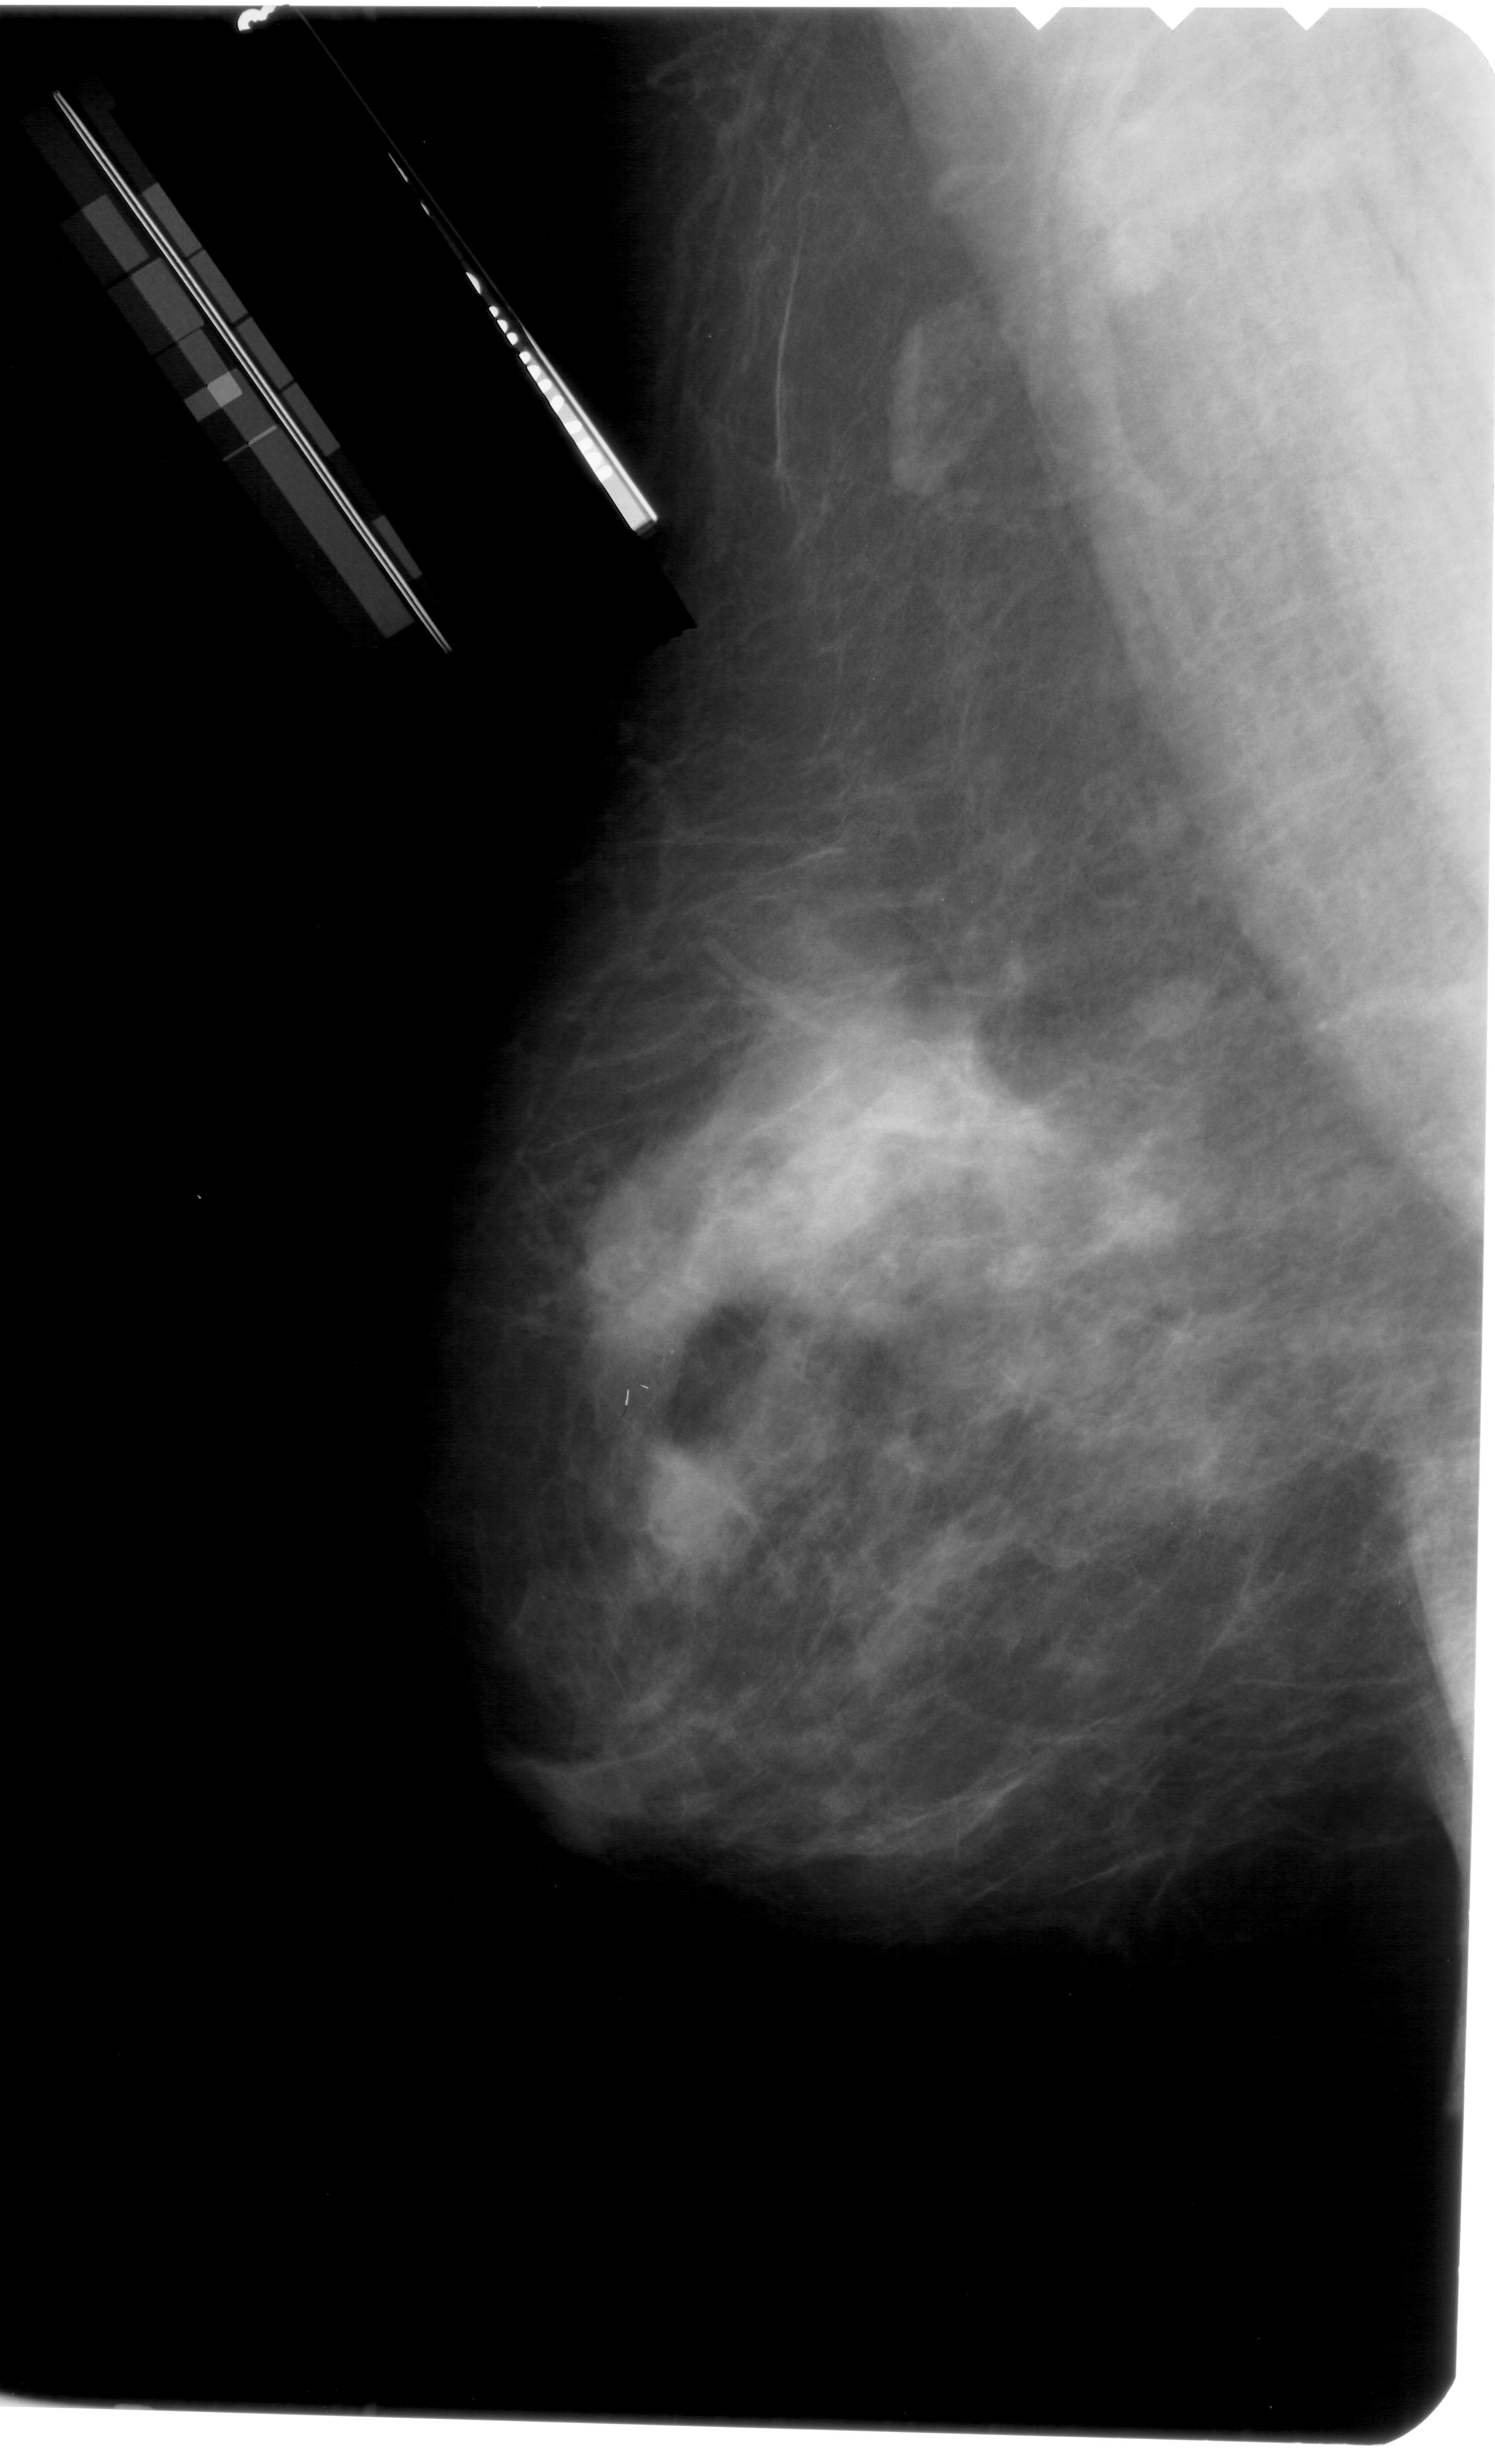
Digitized screen-film mammogram. Left breast. MLO view. 1495 × 2464 image matrix.
Expert-marked regions of interest on this image (one box per marked abnormality):
- calcifications, morphology pleomorphic, distribution clustered; BI-RADS assessment category 4; pathology result (as recorded, not read from the image): benign: bounding box (x1, y1, x2, y2) in pixels: (761, 1129, 903, 1234)